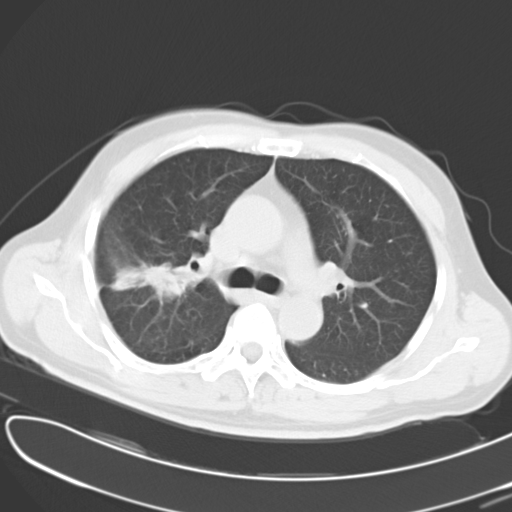
Chest CT, one axial slice. Slice 24 of 37 in the series (ordered by position). Reconstruction kernel B40f. Lung window (W 1500 / L -600 HU). 512 × 512 image matrix, field of view 353 × 353 mm. Male patient, age 53 years. Case-level facts recorded for this patient, not image findings: clinical TNM (as recorded): T2 N1 M0.
Structures marked on this image (bounding box drawn by a radiologist):
- lung tumour (recorded histology: adenocarcinoma): bounding box (x1, y1, x2, y2) in pixels: (94, 241, 191, 303)